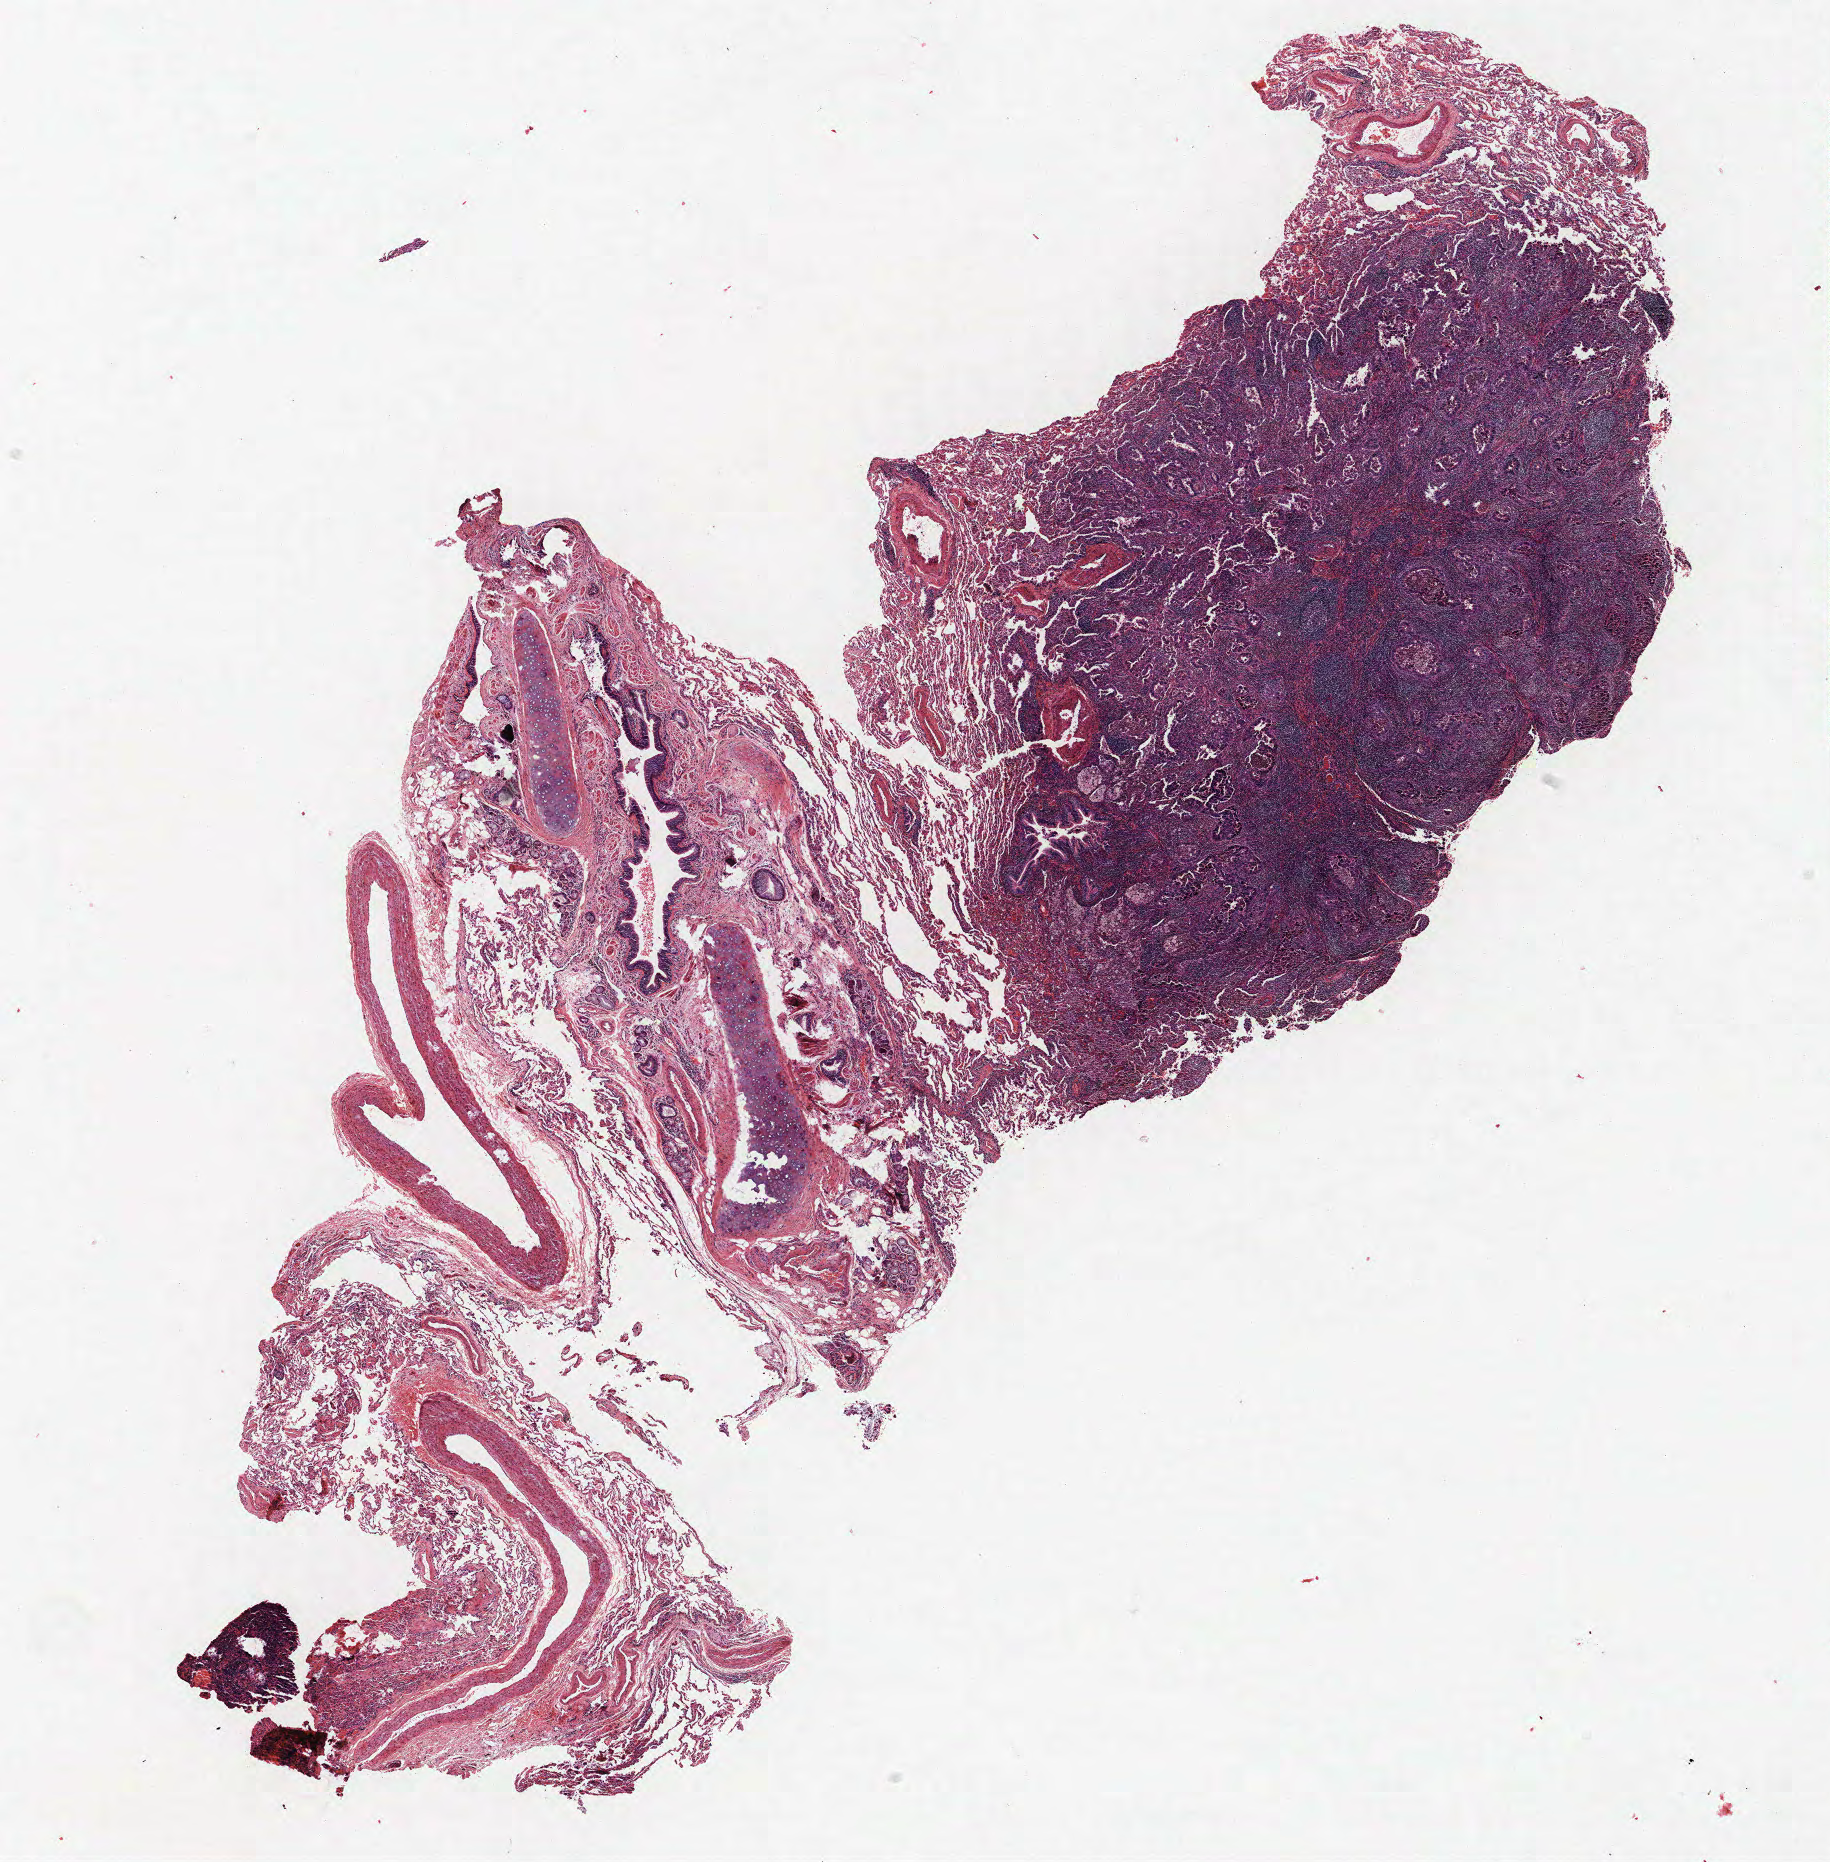
Whole-slide histology image, Hematoxylin and eosin (H&E) stained, whole scanned area (about 14.6 x 14.9 mm, from a 40x scan) shown as a low-resolution overview; FFPE section; lung tissue. Male, age 55 at enrolment. Former smoker at enrolment. Grade: moderately differentiated (G2).
• primary tumour location (clinical record): right upper lobe
• tumour size (pathology): 15 mm
• participant's lung-cancer diagnosis: Acinar cell carcinoma (ICD-O-3 8550/3)
• stage (AJCC 6th edition): IA
• ICD-O-3 topography: upper lobe of lung (C34.1)
• note: participant had 2 primary lung cancers recorded; fields above describe the first